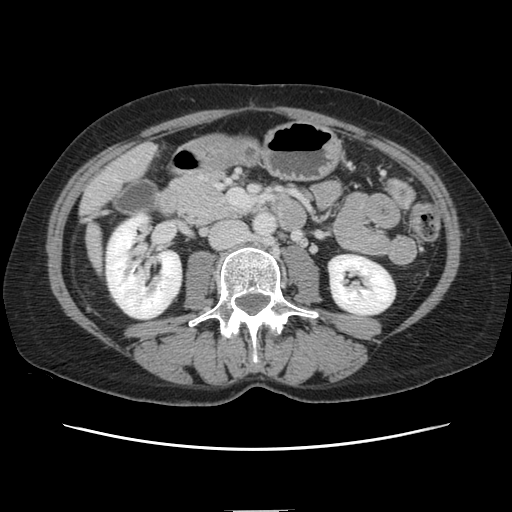
Contrast-enhanced abdominal CT, one axial slice. Position 35 of 141 along the scan axis. 120 kVp. Intravenous contrast given. Soft-tissue window (W 400 / L 40 HU). 2.5 mm slice thickness. 512 × 512 image matrix, field of view 350 × 350 mm. Female patient, age 63 years. From the clinical record (not read from this slice): diagnosis: colorectal cancer liver metastases, imaged before liver resection; multiple liver metastases: yes; largest metastasis: 3.2 cm; disease in both lobes: yes.
Annotated regions visible in this slice (outlined manually by an expert reader):
- liver: bounding box (x1, y1, x2, y2) in pixels: (84, 144, 155, 269)